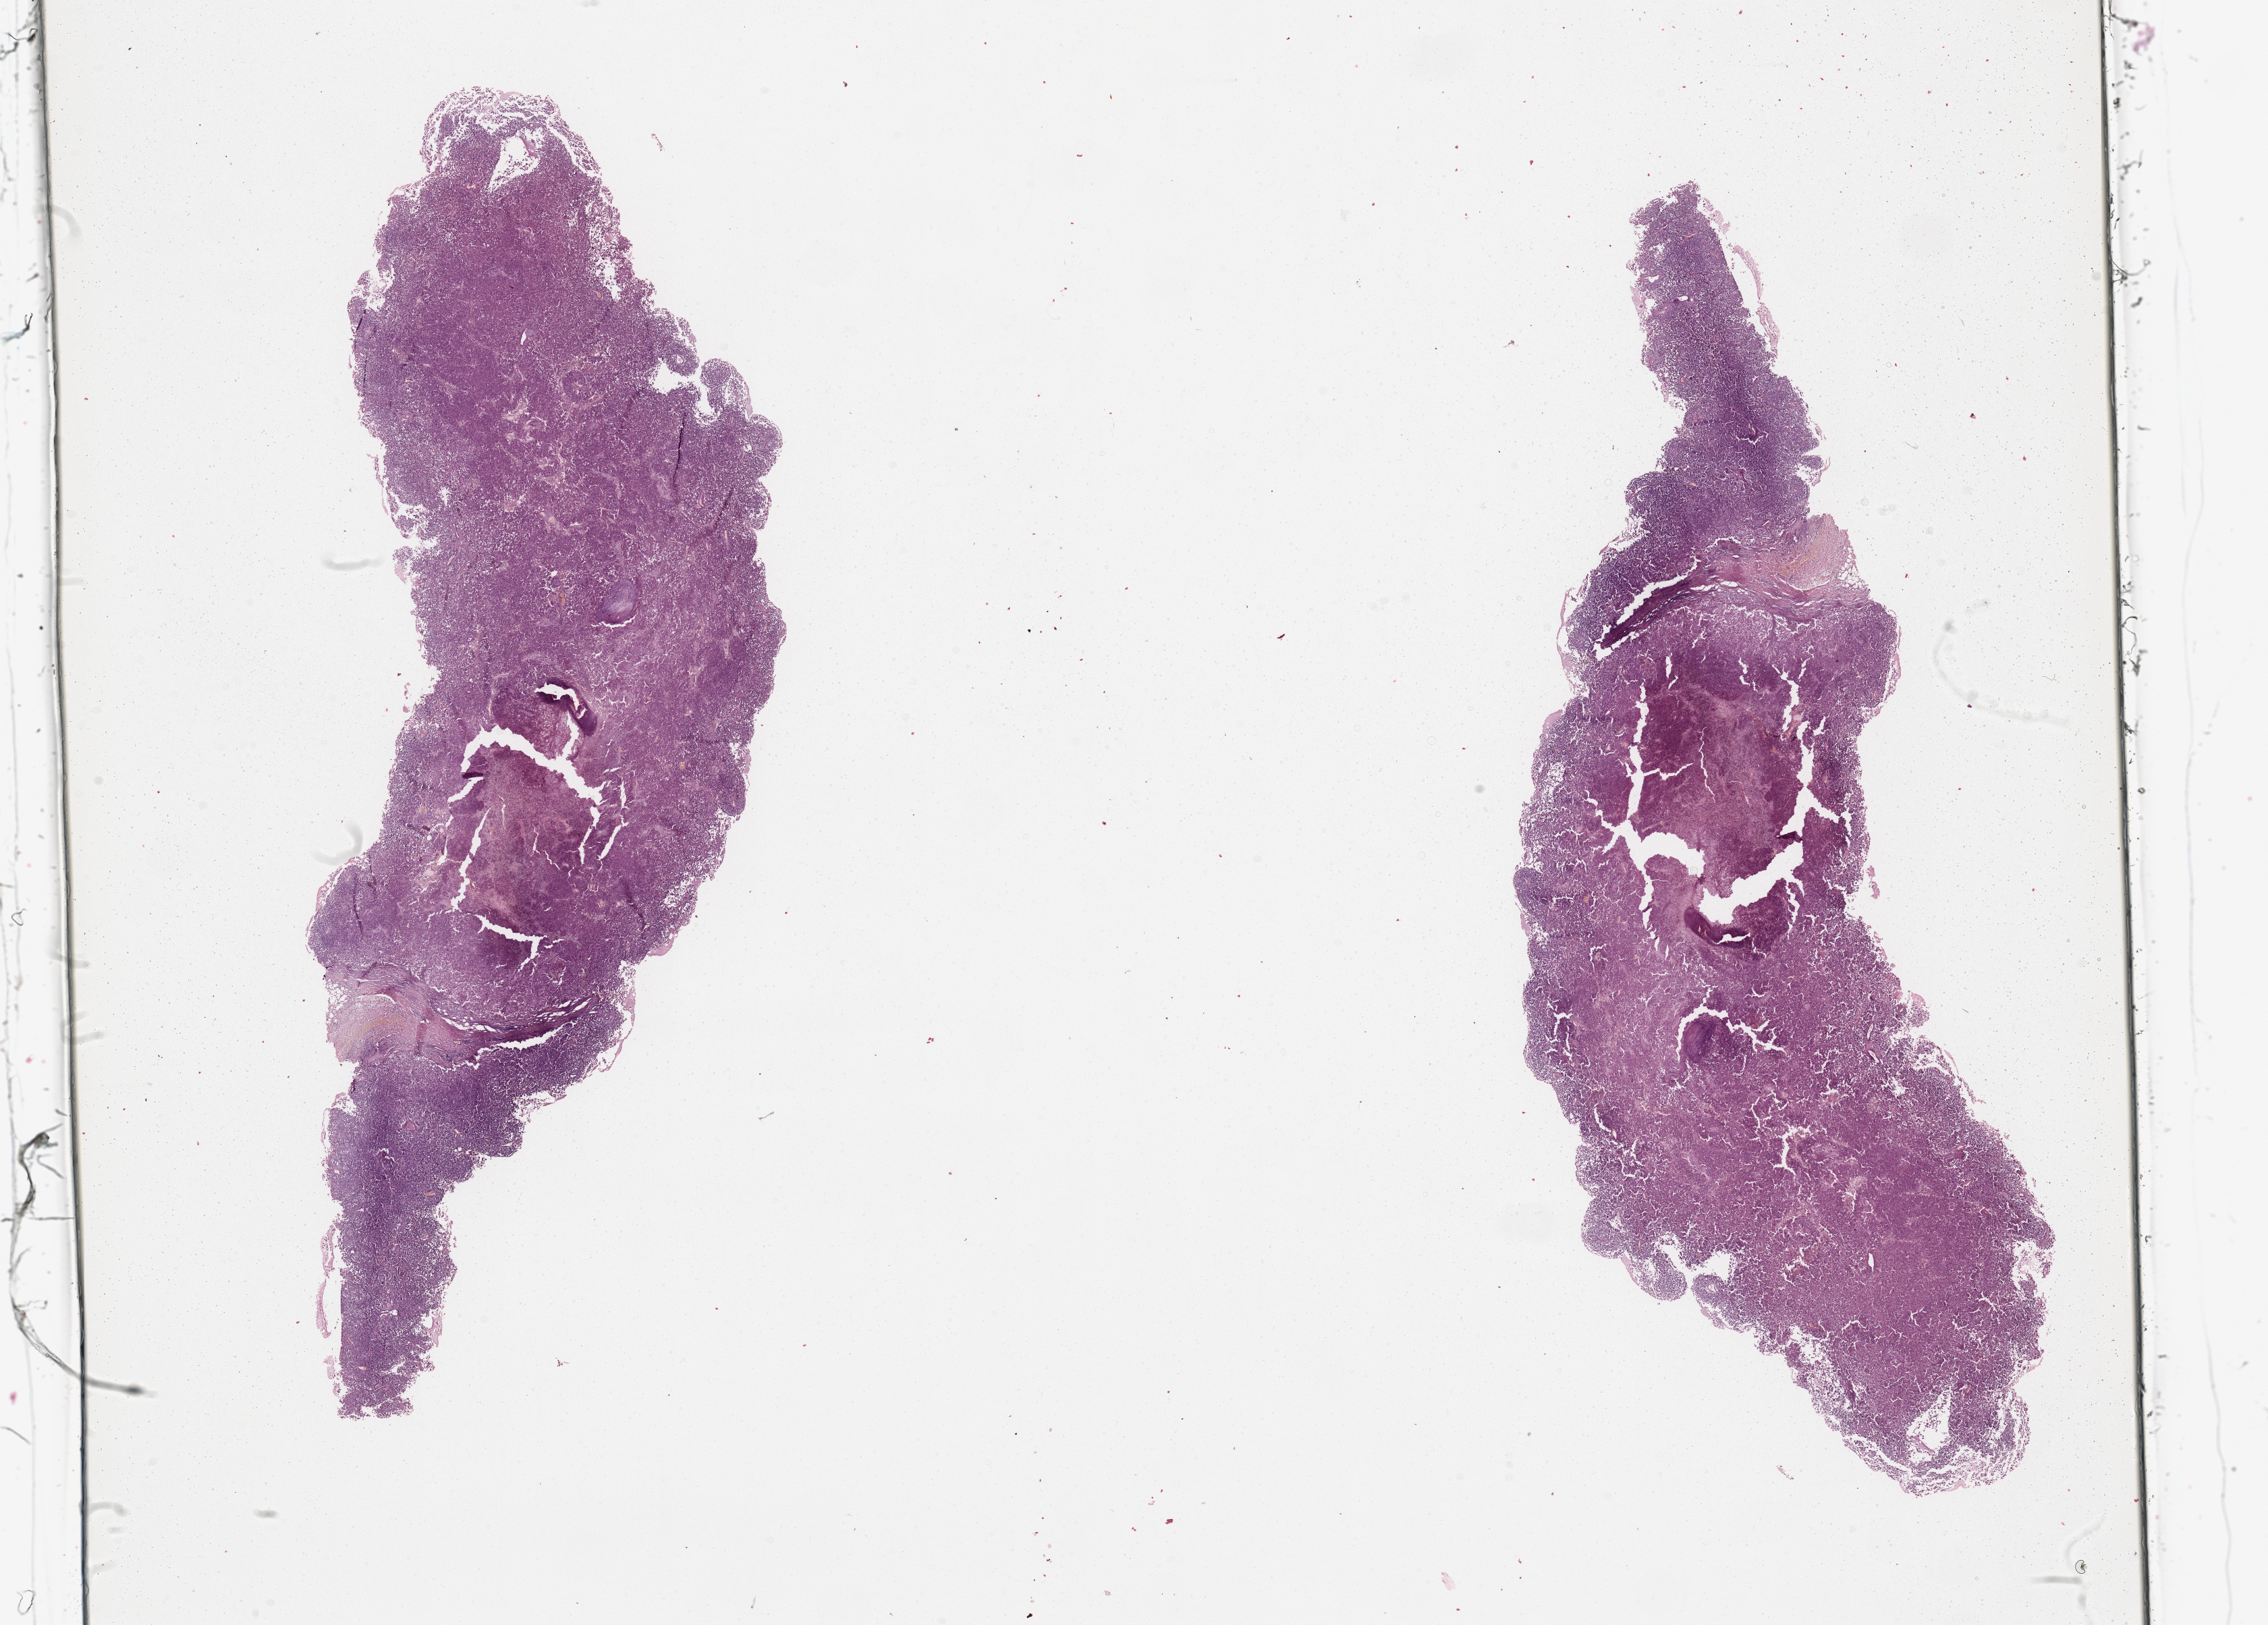
H&E-stained whole-slide image, shown as a low-resolution overview of the whole scanned area (about 26.6 x 19.0 mm, slide scanned at 20x). Tumour tissue sample, sampled site: shoulder. 45-year-old female patient. Composition of this section per pathologist review: tumour nuclei 85%, necrosis 3%.
- this section: metastatic tumour tissue
- patient diagnosis: Malignant melanoma, NOS